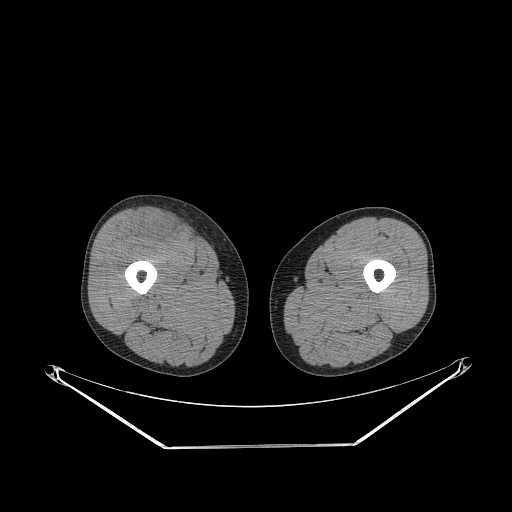
CT of an extremity soft-tissue mass (from a PET/CT study), one axial slice; position 258 of 311 along the scan axis; 140 kVp; soft-tissue window (W 400 / L 40 HU); 3.75 mm slice thickness; 512 × 512 image matrix. Male patient. Case-level facts recorded for this patient, not image findings: histological type: pleiomorphic leiomyosarcoma; grade: intermediate; site of the primary tumour: right thigh.
Structures marked on this image (expert contour drawn on MRI and transferred to this co-registered scan by the dataset authors):
- gross tumour volume including surrounding oedema: bounding box <133,212,181,241> (left, top, right, bottom; pixels)